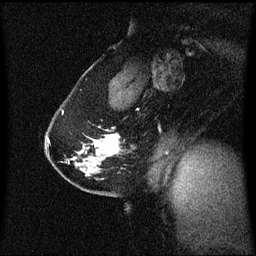
Breast MRI (dynamic contrast-enhanced), one sagittal slice. Position 42 of 60 along the scan axis. Dynamic contrast-enhanced series, image 2 of 3 at this slice position (ordered by acquisition). 1.5 T. TE 4.2 ms, TR 8.4 ms. 256 × 256 image matrix. Female patient, age 40 years. Case-level facts recorded for this patient, not image findings: setting: breast cancer imaged before/during neoadjuvant chemotherapy; receptor status: triple-negative.
Outlined on this slice (semi-automatically segmented with operator editing):
- analysis volume of interest (the breast-tissue region the enhancement analysis was run in; not a lesion): bounding box <46,112,121,188> (left, top, right, bottom; pixels)
- tumour enhancement mask (voxels above the 70 % enhancement threshold inside the analysis volume of interest): <95,135,120,150>